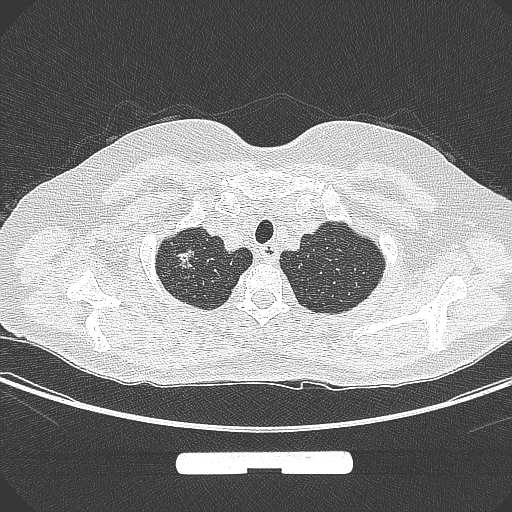
Chest CT, one axial slice. Slice 262 of 295 in the series (ordered by position). 120 kVp. Lung window (W 1500 / L -600 HU). 1 mm slice thickness. 512 × 512 image matrix, field of view 369 × 369 mm. Female patient, age 58 years. Case-level facts recorded for this patient, not image findings: clinical TNM (as recorded): T1b N0 M0; histopathological grade: G2-3.
Annotated regions visible in this slice (rectangle marked by the reading radiologist):
- lung tumour (recorded histology: adenocarcinoma): bounding box <174,243,201,280> (left, top, right, bottom; pixels)